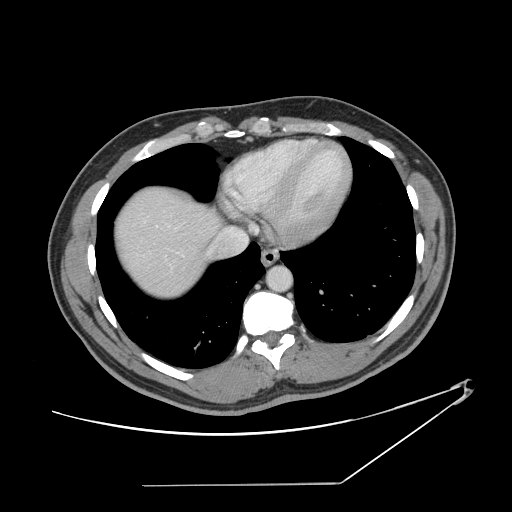
Contrast-enhanced abdominal CT, one axial slice. Slice 134 of 152 in the series (ordered by position). Reconstruction kernel STANDARD. Intravenous contrast given. Soft-tissue window (W 400 / L 40 HU). 2.5 mm slice thickness. 512 × 512 image matrix, field of view 432 × 432 mm. Male patient, age 45 years. From the clinical record (not read from this slice): diagnosis: colorectal cancer liver metastases, imaged before liver resection; multiple liver metastases: no; largest metastasis: 1 cm; disease in both lobes: no.
Outlined on this slice (outlined manually by an expert reader):
- hepatic veins: bounding box (x1, y1, x2, y2) in pixels: (156, 226, 248, 247)
- liver: (116, 189, 219, 298)
- planned liver remnant (the part of the liver to remain after resection): (116, 189, 219, 298)